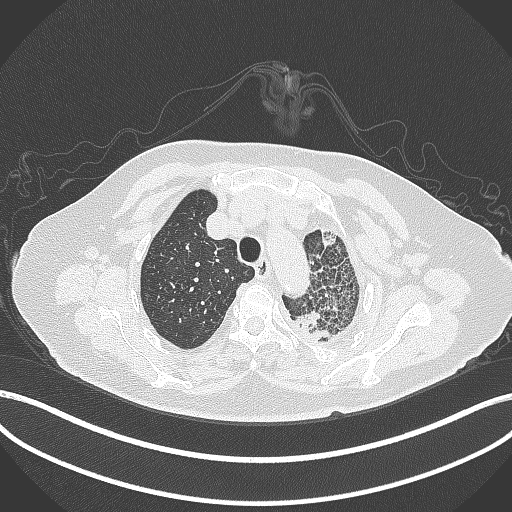
Chest CT, one axial slice. Position 320 of 399 along the scan axis. Reconstruction kernel B70f. Lung window (W 1500 / L -600 HU). 512 × 512 image matrix. Female patient, age 75 years. From the clinical record (not read from this slice): clinical TNM (as recorded): T3 N3 M1.
Outlined on this slice (rectangle marked by the reading radiologist):
- lung tumour (recorded histology: adenocarcinoma): bounding box <293,305,335,345> (left, top, right, bottom; pixels)